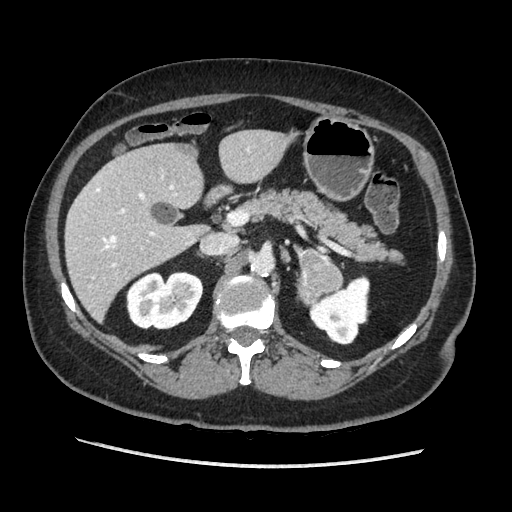
Contrast-enhanced abdominal CT, one axial slice; position 114 of 203 along the scan axis; soft-tissue window (W 400 / L 40 HU); 1.25 mm slice thickness; 512 × 512 image matrix. Female patient. Case-level facts recorded for this patient, not image findings: diagnosis: adrenocortical carcinoma; tumour side: left adrenal; tumour size at pathology: 6.5 cm; Ki-67 index: 22 %; stage (as recorded): 2.
Outlined on this slice (semi-automatically segmented with operator editing):
- mass: box from (x=300, y=250) to (x=342, y=302) px